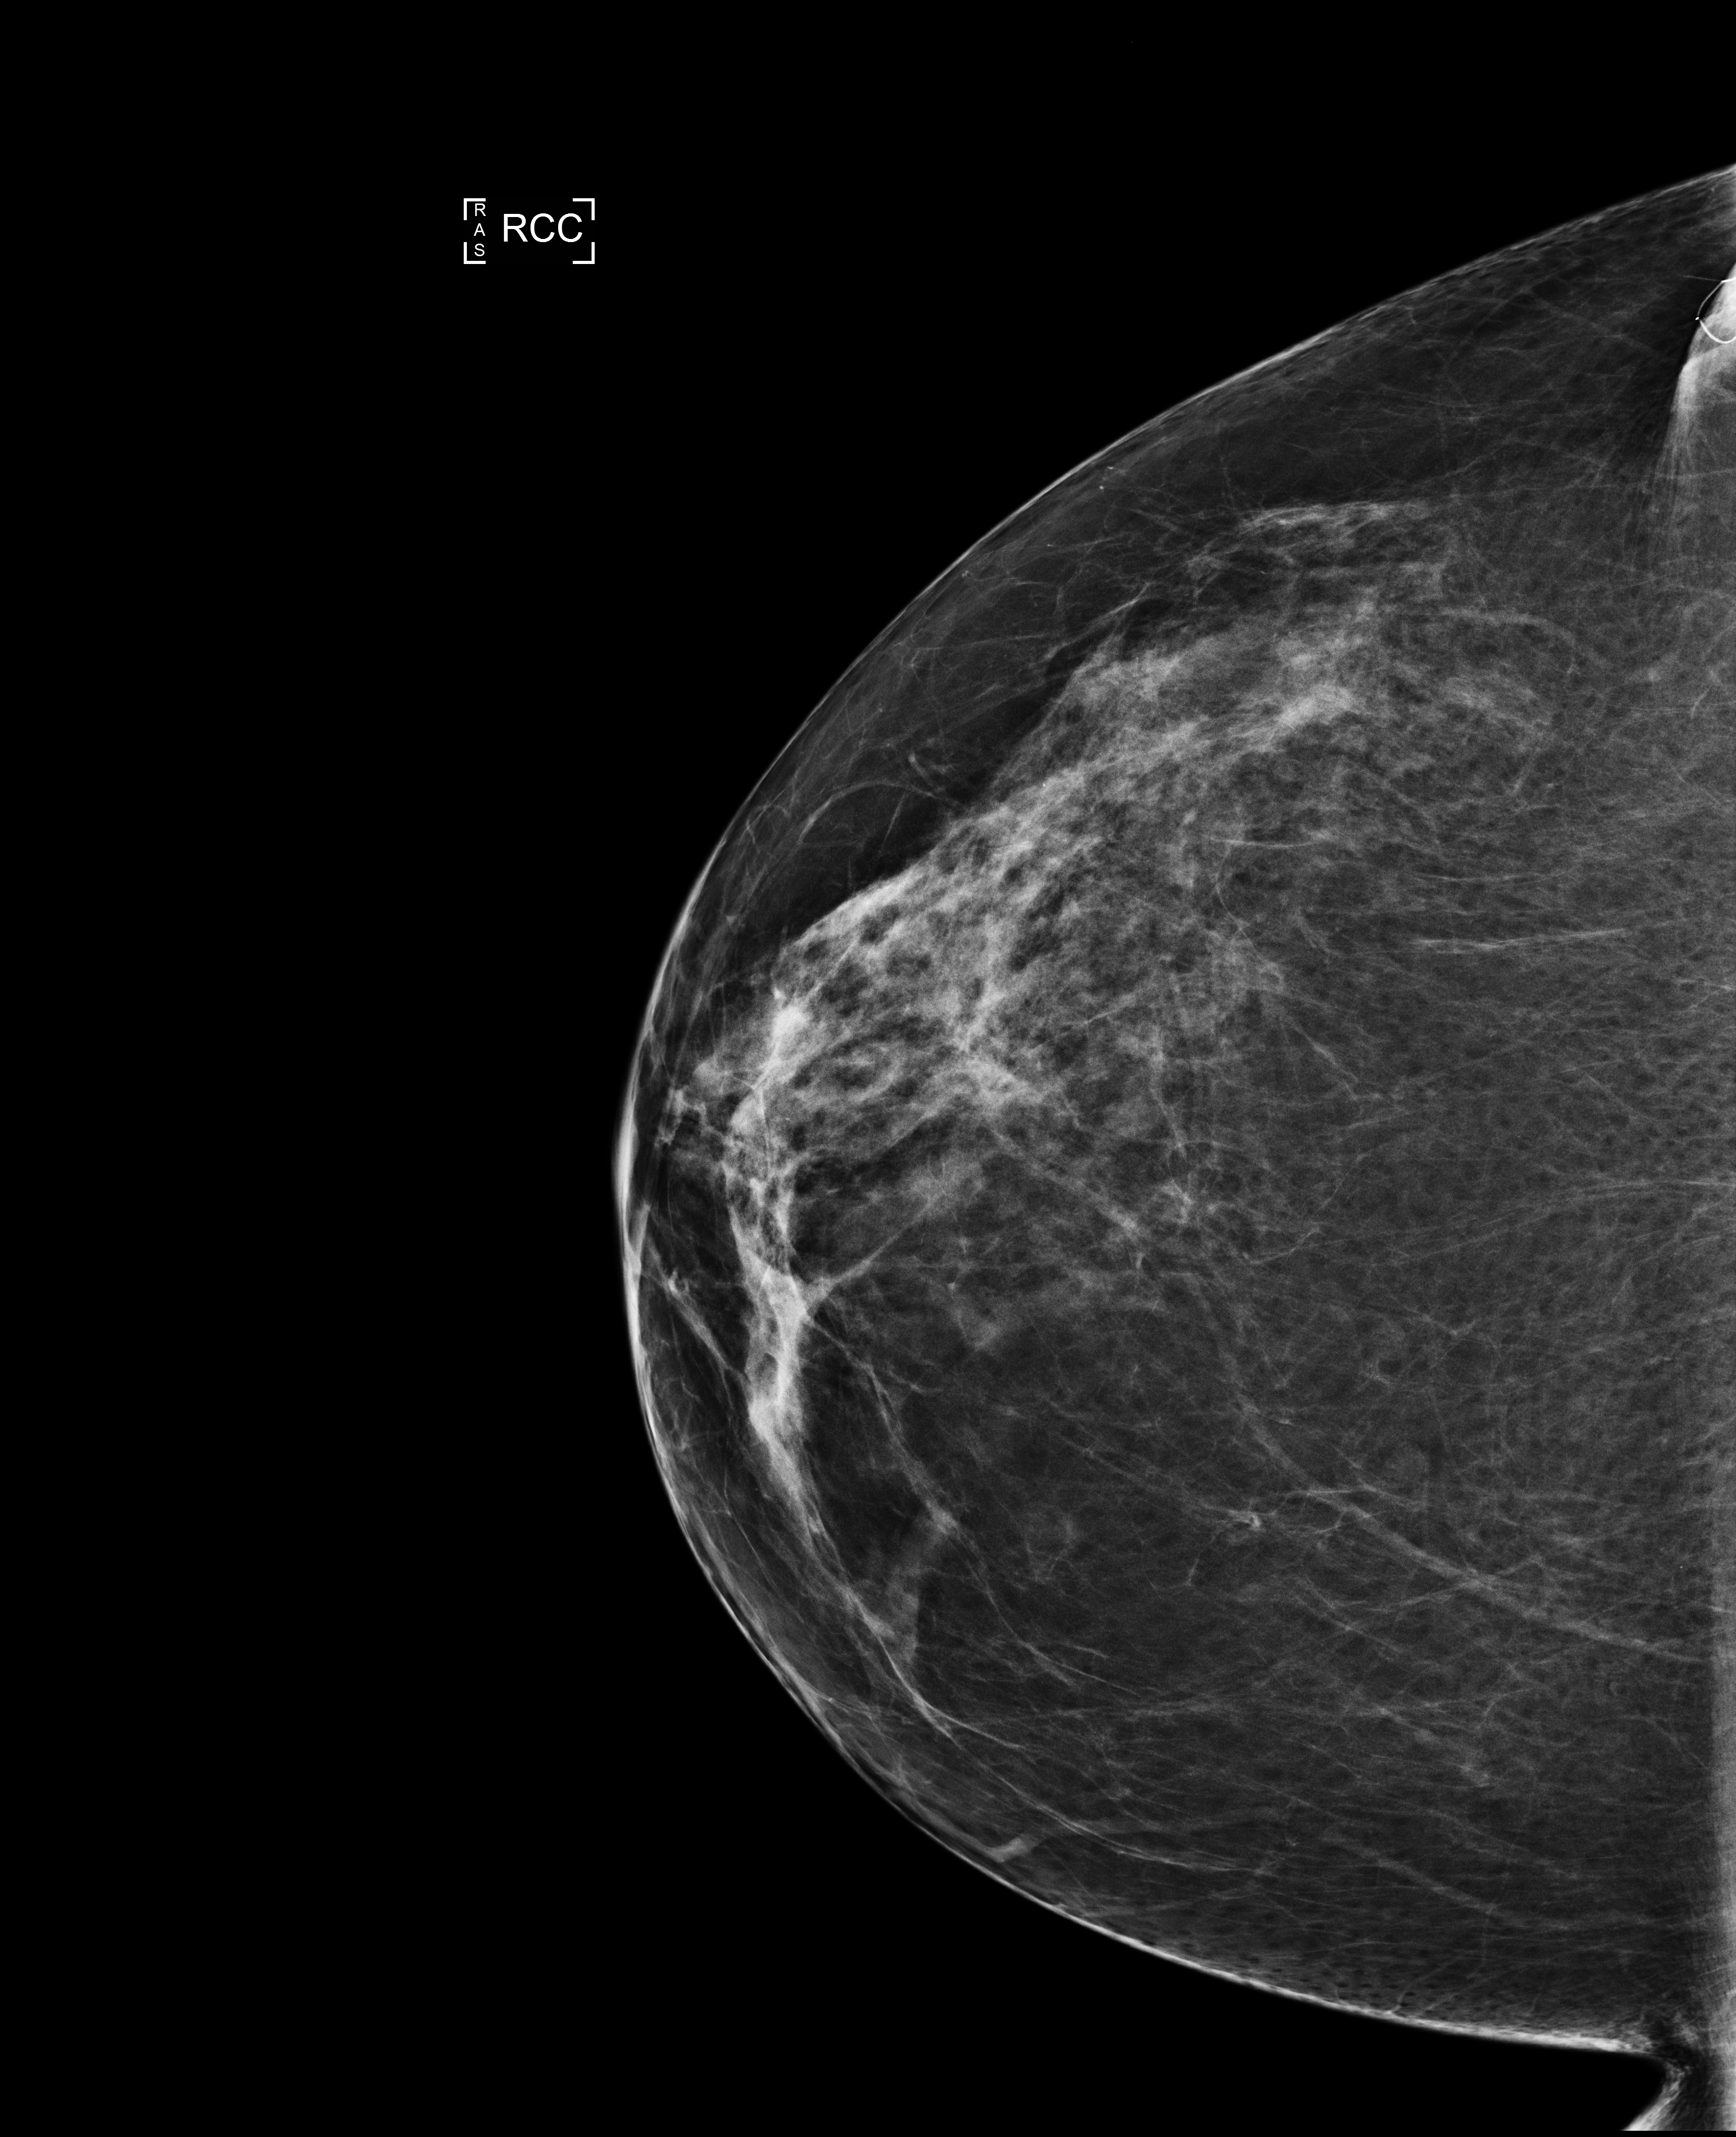
Full-field digital mammogram (FFDM), right breast, cranio-caudal projection, annual screening mammography examination, system: Selenia Dimensions. Patient: female, 66 years.
- BI-RADS breast density category at the screening exam (both breasts, scale 1–4): 2
- final BI-RADS category for the screening round (tomosynthesis exam, both breasts): category 1
- recall: no recall after this screen